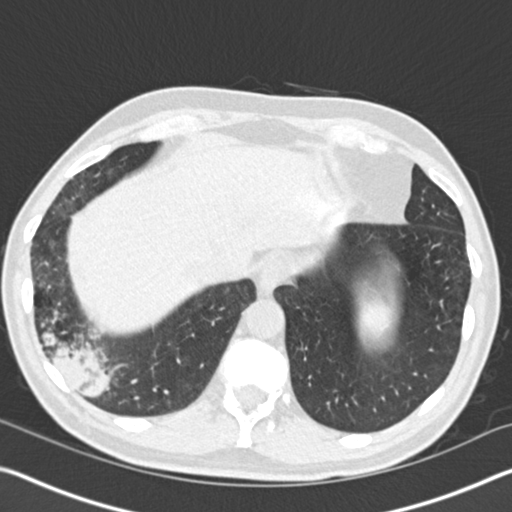
Axial slice from a low-dose chest CT screening exam; baseline annual screen; lung window (W 1500 / L -600 HU); 2 mm slice thickness; slice 125 of 161 in the series; 512 × 512 image matrix, field of view 340 × 340 mm. Male participant, aged 61 years at enrolment.
Expert reader's lesion annotation, bounding box (x1, y1, x2, y2) in pixels: (10, 274, 137, 414). Screening reader's record for this exam (one nodule recorded; not confirmed to be the boxed lesion): non-calcified nodule or mass ≥4 mm, right lower lobe, 52 × 36 mm, spiculated (stellate) margins, soft tissue attenuation. Official screen result: positive, change unspecified: nodule(s) >= 4 mm or enlarging nodule(s), mass(es), or other non-specific abnormalities suspicious for lung cancer. Later outcome: lung cancer diagnosed 392 days after this screen — bronchiolo-alveolar adenocarcinoma, NOS, right lower lobe, moderately differentiated (G2), stage IIIB (AJCC 6th edition), 90 mm at pathology.